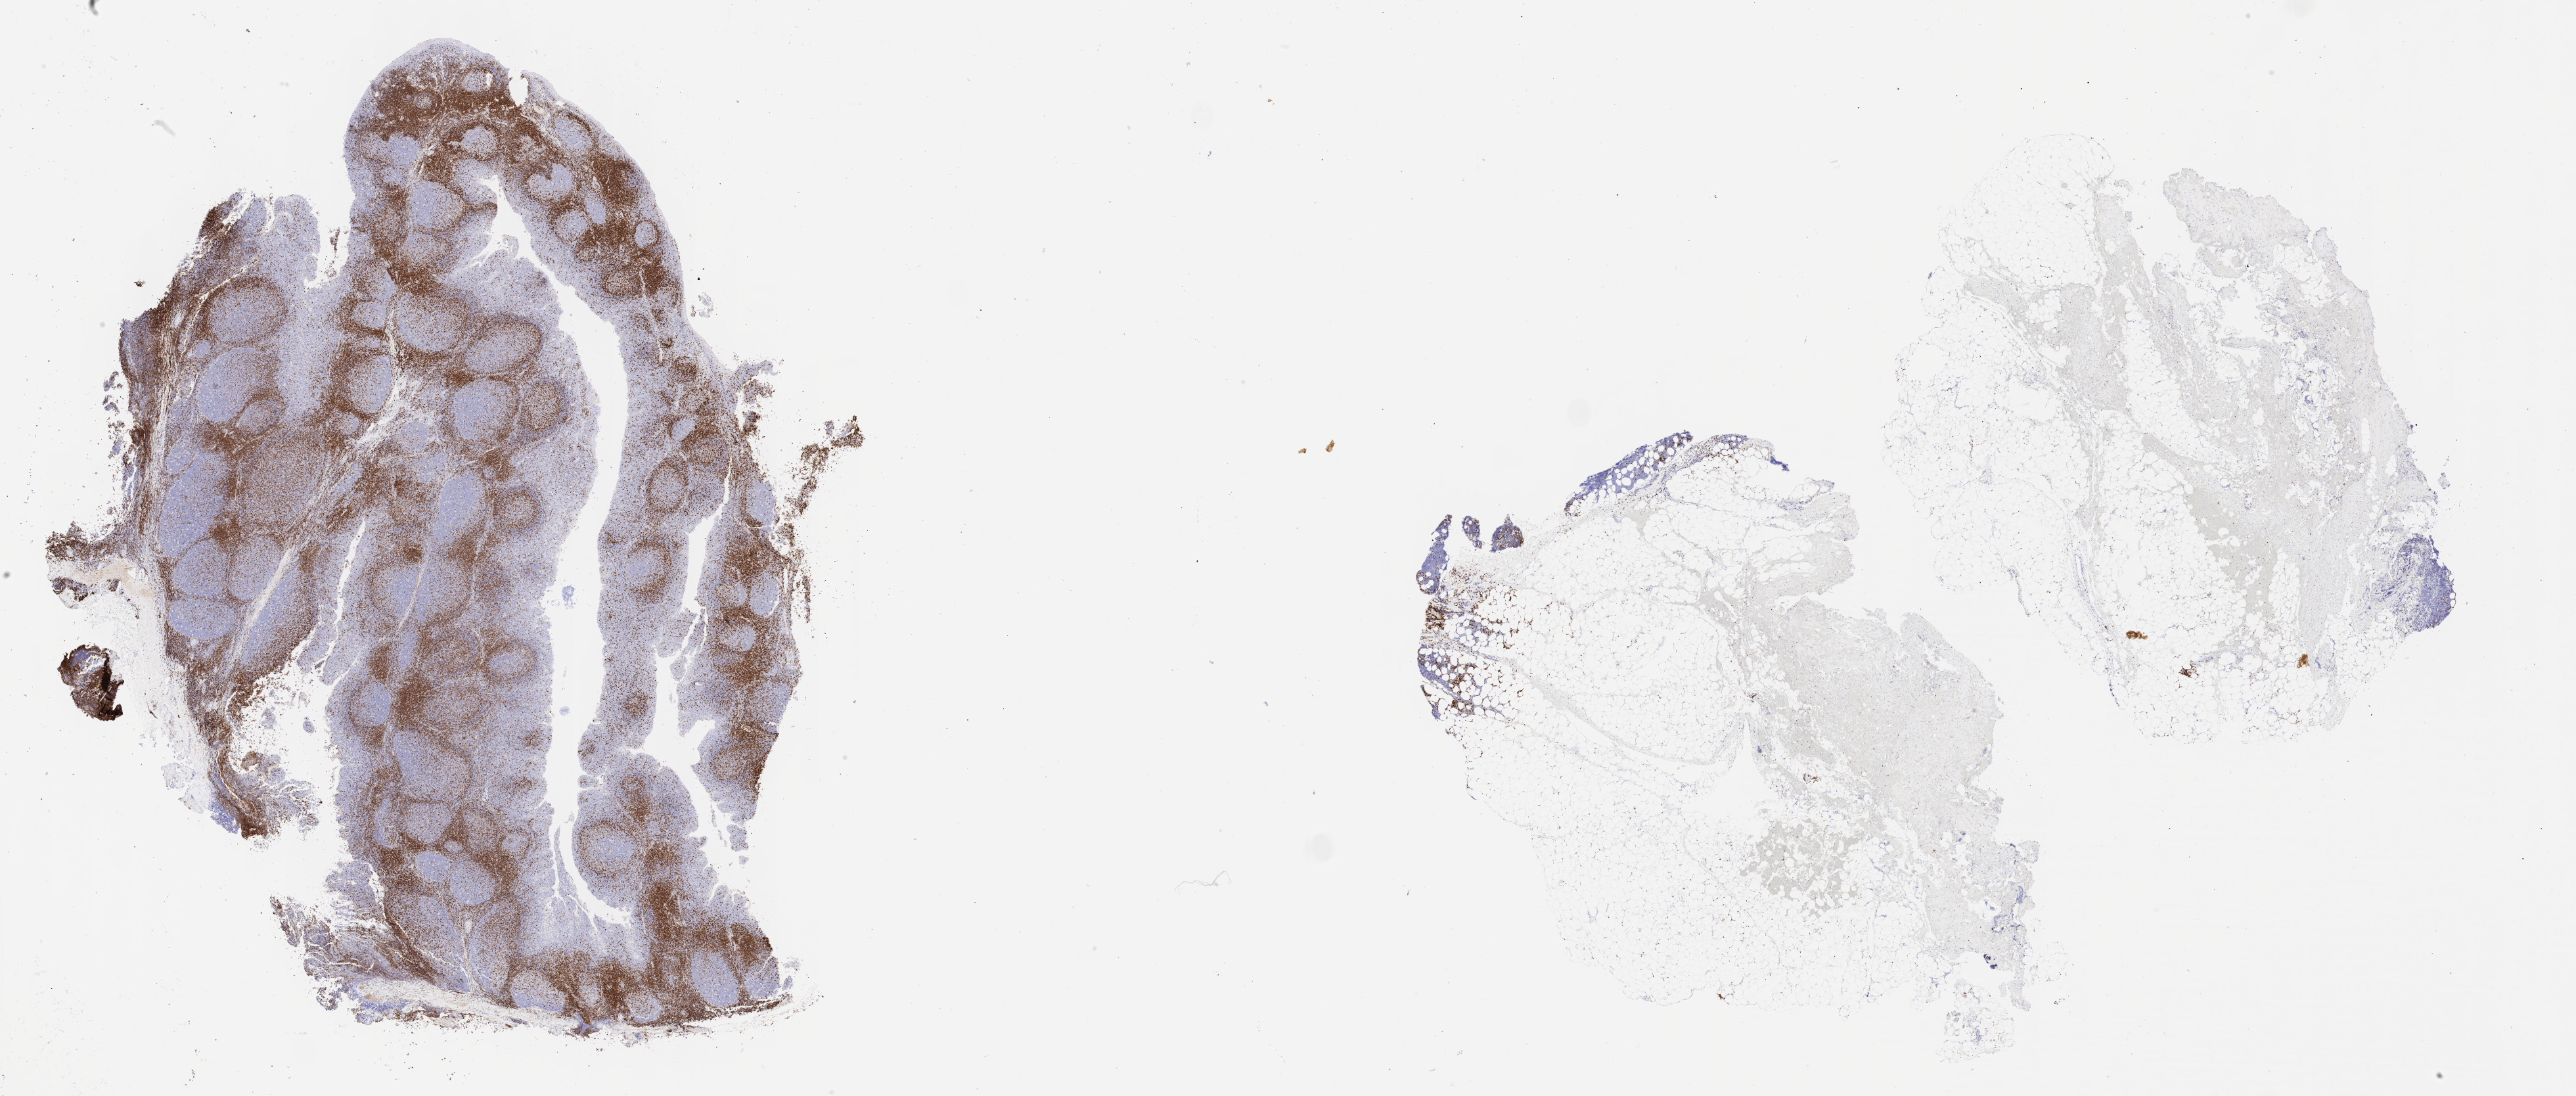
Whole-slide image, immunohistochemical stain for CD3, whole scanned area (about 31.7 x 13.5 mm) shown as a low-resolution overview; specimen: tumor tissue; anatomic site: upper limb lymph node. Patient: male, age 76 years.
Diagnosis: Burkitt lymphoma, NOS.